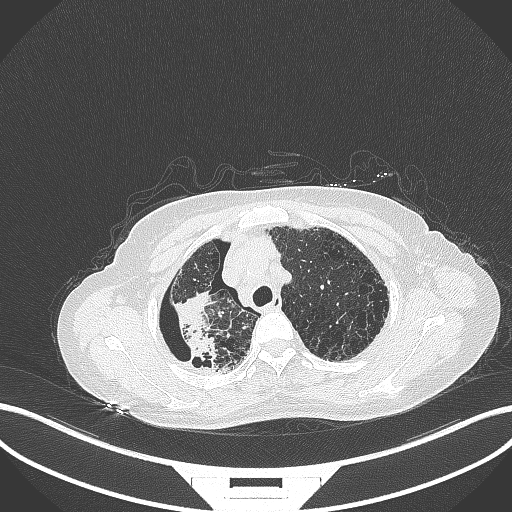
Chest CT, one axial slice; slice 289 of 408 in the series (ordered by position); reconstruction kernel B70f; lung window (W 1500 / L -600 HU); 1 mm slice thickness; 512 × 512 image matrix, field of view 400 × 400 mm. Female patient, age 64 years. From the clinical record (not read from this slice): clinical TNM (as recorded): T3 N3 M0.
Structures marked on this image (rectangle marked by the reading radiologist):
- lung tumour (recorded histology: squamous cell carcinoma): box from (x=168, y=284) to (x=219, y=371) px